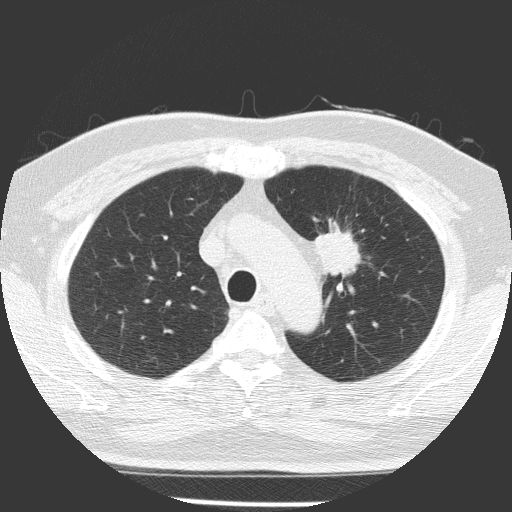
Low-dose screening chest CT, one axial slice; position 114 of 156 along the scan axis; reconstruction kernel FC51; 120 kVp; lung window (W 1500 / L -600 HU); 2 mm slice thickness; 512 × 512 image matrix, field of view 309 × 309 mm.
Structures marked on this image (expert manual segmentation):
- lesion 1 (tumor, upper lobe of left lung): bounding box (x1, y1, x2, y2) in pixels: (315, 227, 360, 276)